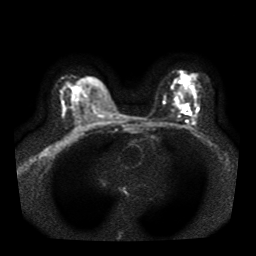
Breast MRI, one axial slice. Position 23 of 41 along the scan axis. Diffusion-weighted series; image 2 of 4 stored at this slice position (different b-values; order by instance number). 1.5 T. 256 × 256 image matrix. Female patient.
Outlined on this slice (manually delineated by an expert):
- tumour on diffusion-weighted imaging: bounding box (x1, y1, x2, y2) in pixels: (181, 106, 190, 110)